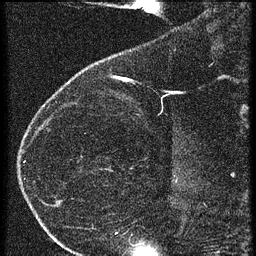
Breast MRI (dynamic contrast-enhanced), one sagittal slice. Slice 15 of 60 in the series (ordered by position). 3 images stored at this slice position (order not interpretable as contrast timing). 1.5 T. TE 4.2 ms, TR 20.4 ms. 1.5 mm slice thickness. 256 × 256 image matrix, field of view 180 × 180 mm. Female patient, age 35 years. From the clinical record (not read from this slice): setting: breast cancer imaged before/during neoadjuvant chemotherapy; receptor status: HR-positive, HER2-negative.
Structures marked on this image (semi-automatically segmented with operator editing):
- analysis volume of interest (the breast-tissue region the enhancement analysis was run in; not a lesion): bounding box [x1, y1, x2, y2] px = [65, 60, 169, 119]
- tumour enhancement mask (voxels above the 90 % enhancement threshold inside the analysis volume of interest): [121, 78, 128, 81]